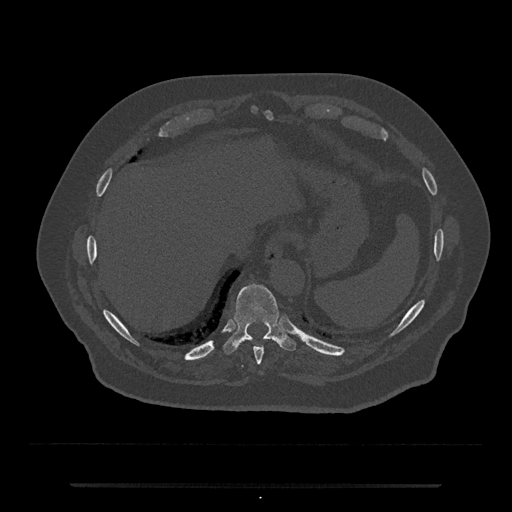
CT including the spine, one axial slice. Position 723 of 797 along the scan axis. Reconstruction kernel Br40s/3. Bone window (W 1800 / L 400 HU). 0.5 mm slice thickness. 512 × 512 image matrix. Male patient, age 80 years. Case-level facts recorded for this patient, not image findings: primary cancer: prostate.
Structures marked on this image (semi-automatically segmented with operator editing):
- T10 vertebra: box from (x=223, y=284) to (x=296, y=355) px
- T9 vertebra: (x=254, y=347)–(x=264, y=366)